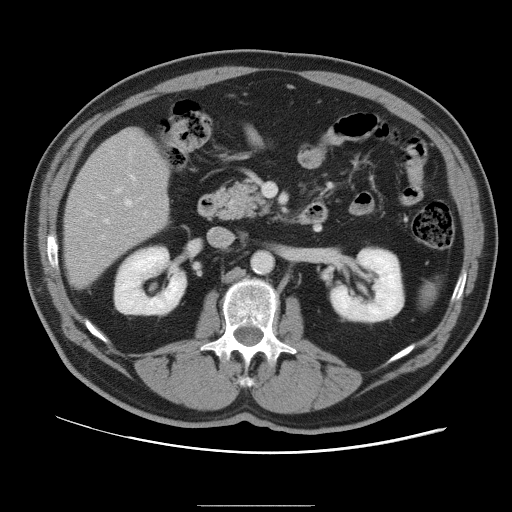
Contrast-enhanced abdominal CT, one axial slice; slice 43 of 105 in the series (ordered by position); 120 kVp; soft-tissue window (W 400 / L 40 HU); 5 mm slice thickness; 512 × 512 image matrix, field of view 399 × 399 mm. Male patient, age 64 years. From the clinical record (not read from this slice): diagnosis: colorectal cancer liver metastases, imaged before liver resection; multiple liver metastases: yes; largest metastasis: 3 cm; disease in both lobes: yes.
Structures marked on this image (expert manual segmentation):
- hepatic veins: bounding box <105,200,132,223> (left, top, right, bottom; pixels)
- liver: <66,129,169,287>
- planned liver remnant (the part of the liver to remain after resection): <67,129,169,287>
- portal vein (with intrahepatic branches): <102,174,136,238>